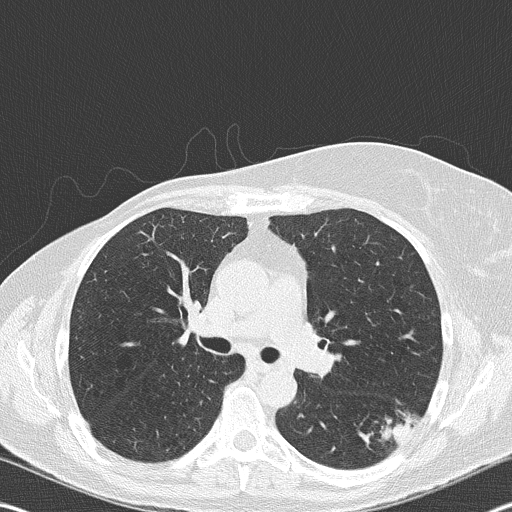
Low-dose screening chest CT, one axial slice; position 112 of 177 along the scan axis; reconstruction kernel B50f; 120 kVp; lung window (W 1500 / L -600 HU); 2 mm slice thickness; 512 × 512 image matrix, field of view 342 × 342 mm.
Annotated regions visible in this slice (outlined manually by an expert reader):
- lesion 1 (tumor): bounding box <383,412,416,445> (left, top, right, bottom; pixels)